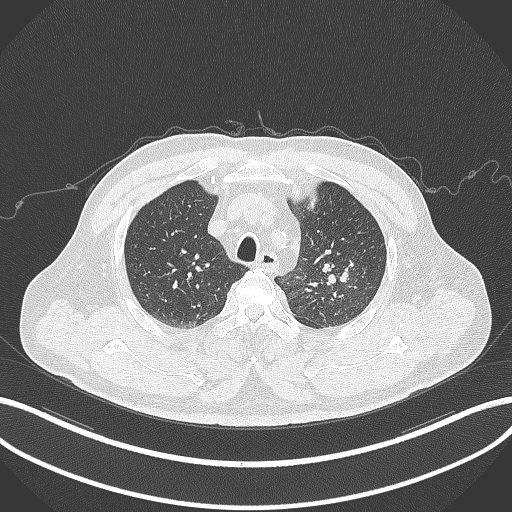
Chest CT, one axial slice; reconstruction kernel B70f; 120 kVp; lung window (W 1500 / L -600 HU); 512 × 512 image matrix, field of view 400 × 400 mm. Patient: male, 67 years. From the clinical record (not read from this slice): clinical TNM (as recorded): T2a N1 M0; histopathological grade: G3.
Outlined on this slice (bounding box drawn by a radiologist):
- lung tumour (recorded histology: adenocarcinoma): bounding box [x1, y1, x2, y2] px = [319, 258, 352, 286]